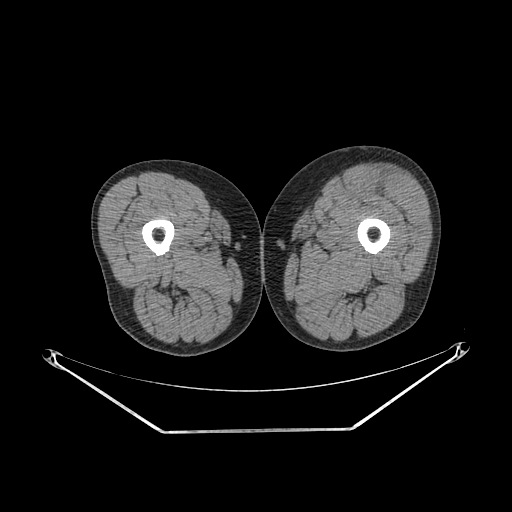
CT of an extremity soft-tissue mass (from a PET/CT study), one axial slice; slice 218 of 267 in the series (ordered by position); reconstruction kernel SOFT; 140 kVp; soft-tissue window (W 400 / L 40 HU); 3.75 mm slice thickness; 512 × 512 image matrix, field of view 500 × 500 mm. Male patient. From the clinical record (not read from this slice): histological type: extraskeletal osteosarcoma; grade: high; site of the primary tumour: thigh.
Outlined on this slice (expert contour drawn on MRI and transferred to this co-registered scan by the dataset authors):
- gross tumour volume (mass): bounding box (x1, y1, x2, y2) in pixels: (383, 176, 398, 202)